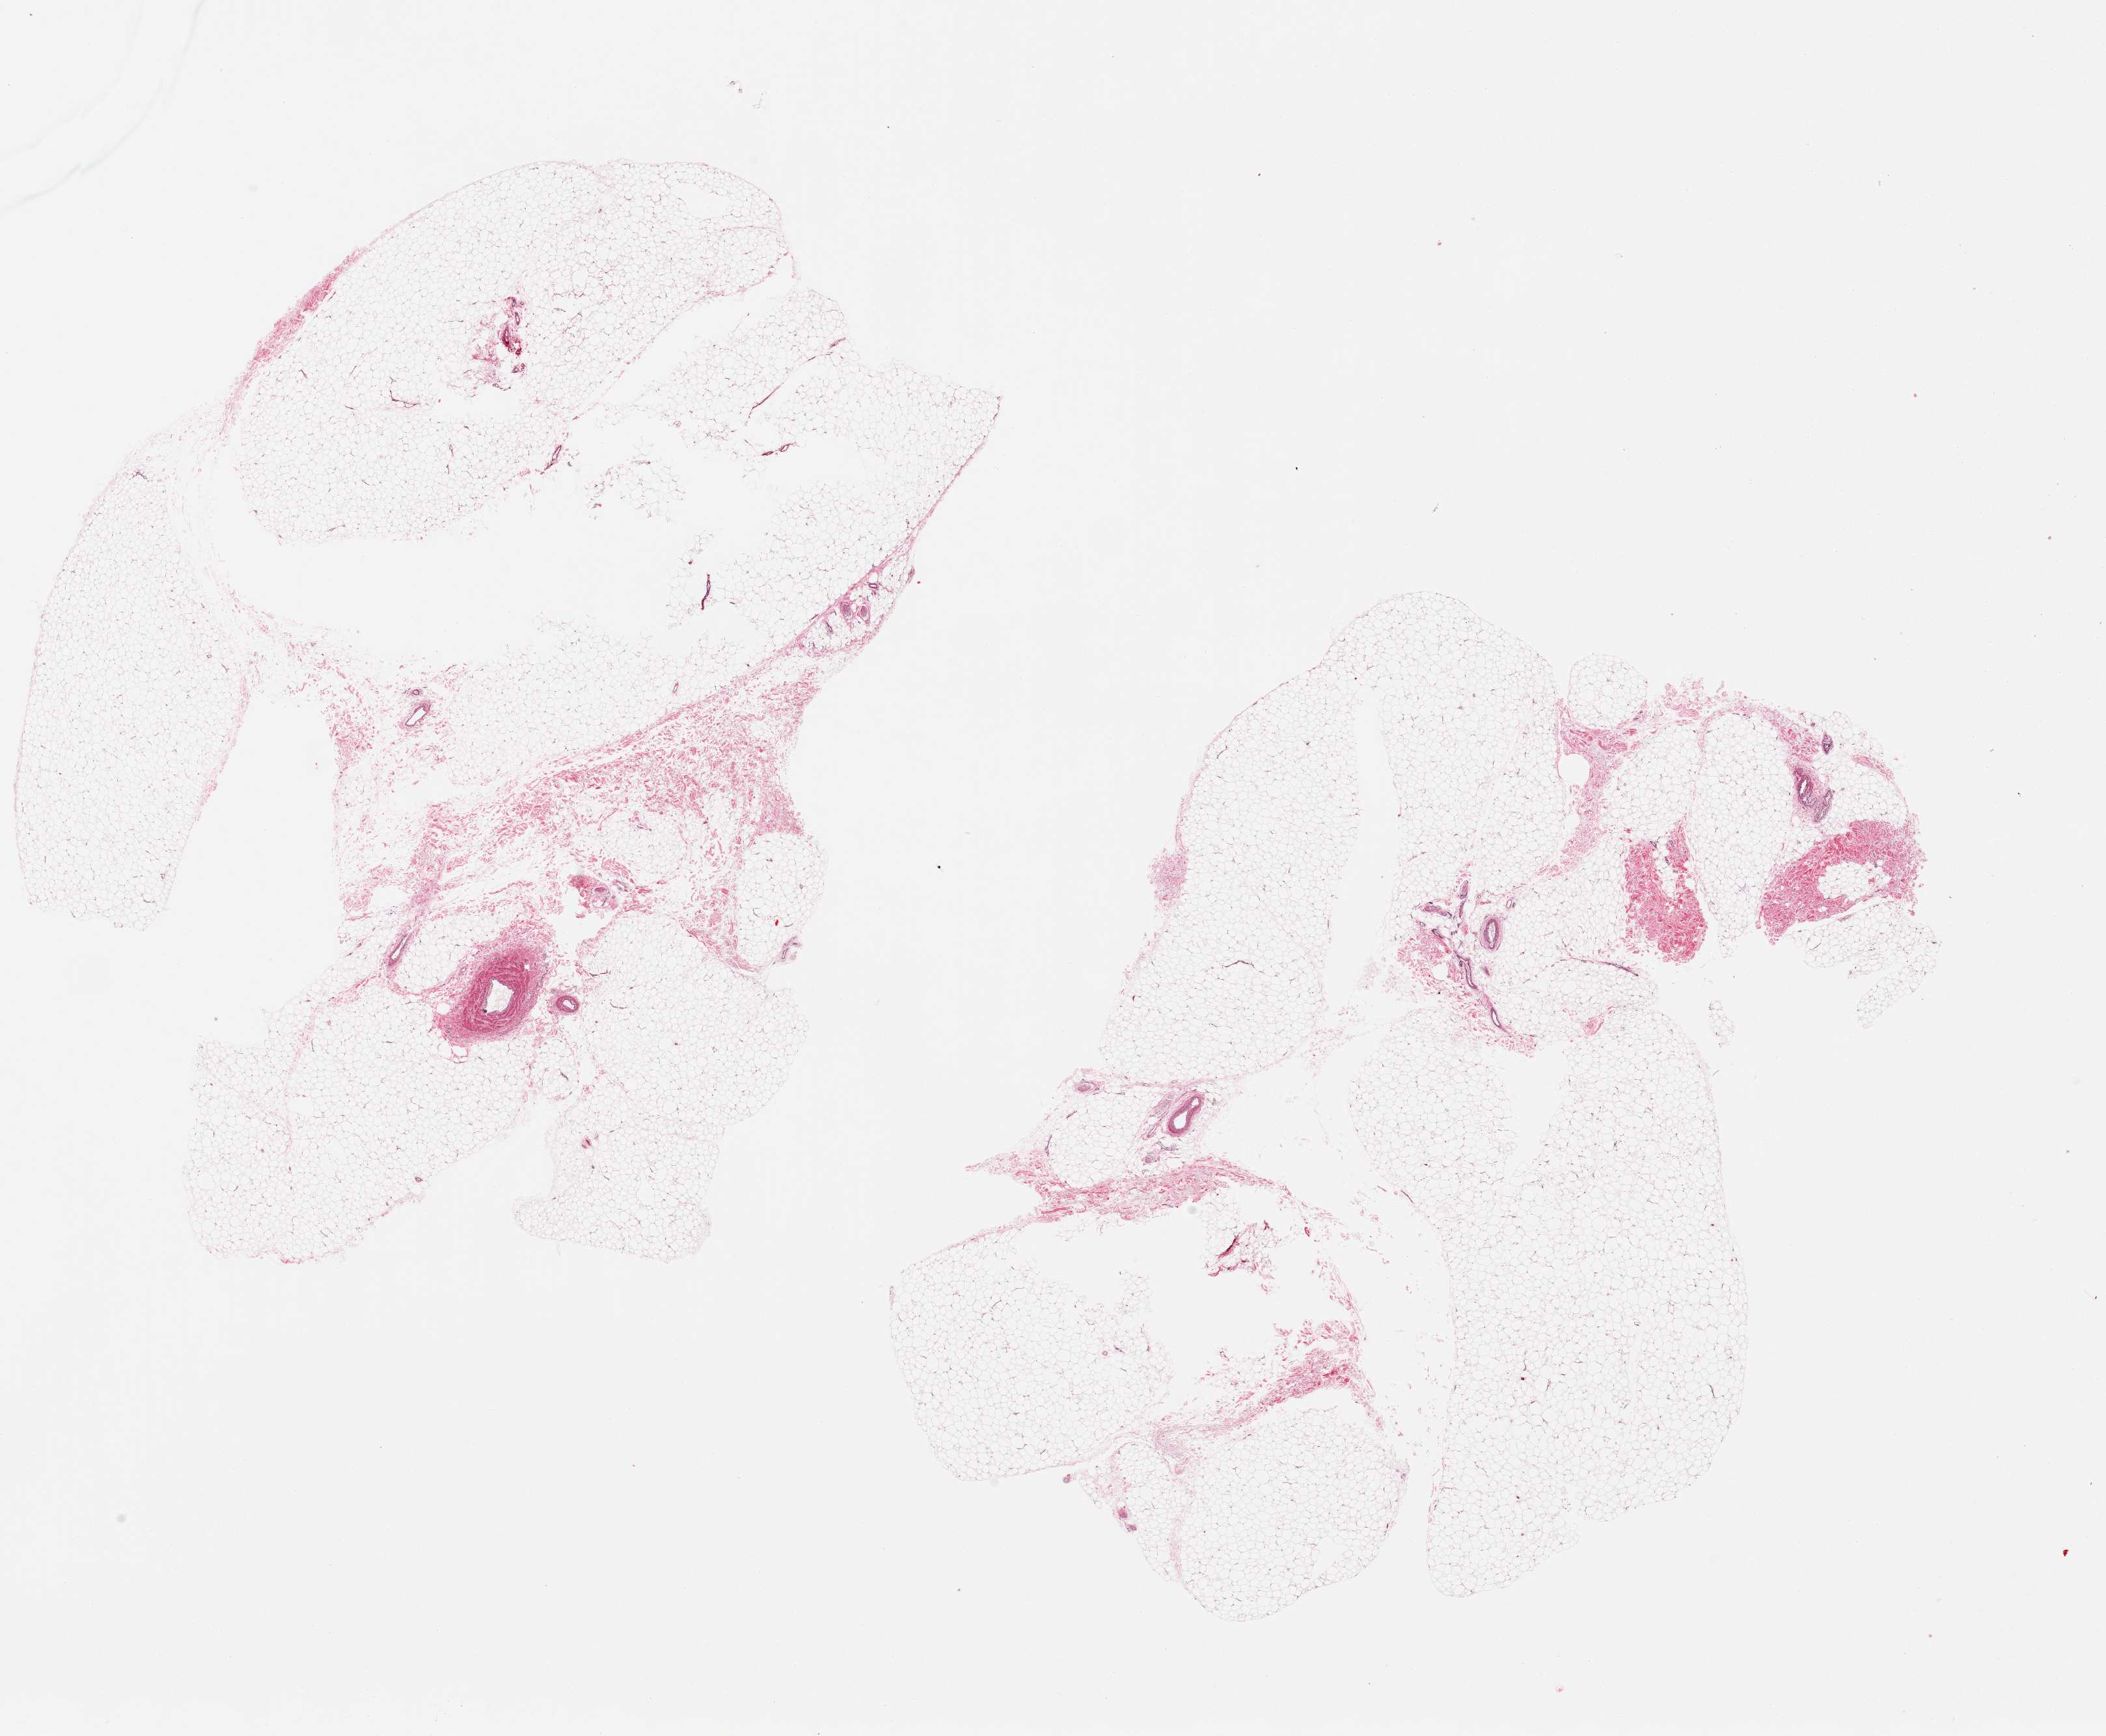
Digitized H&E-stained section — whole scanned area (about 25.6 x 21.1 mm) shown as a low-resolution overview; PAXgene-fixed, paraffin-embedded tissue; target tissue: adipose tissue; donor tissue sample. Male donor.
Review note (as recorded): 2 pieces, both disrupted centrally.